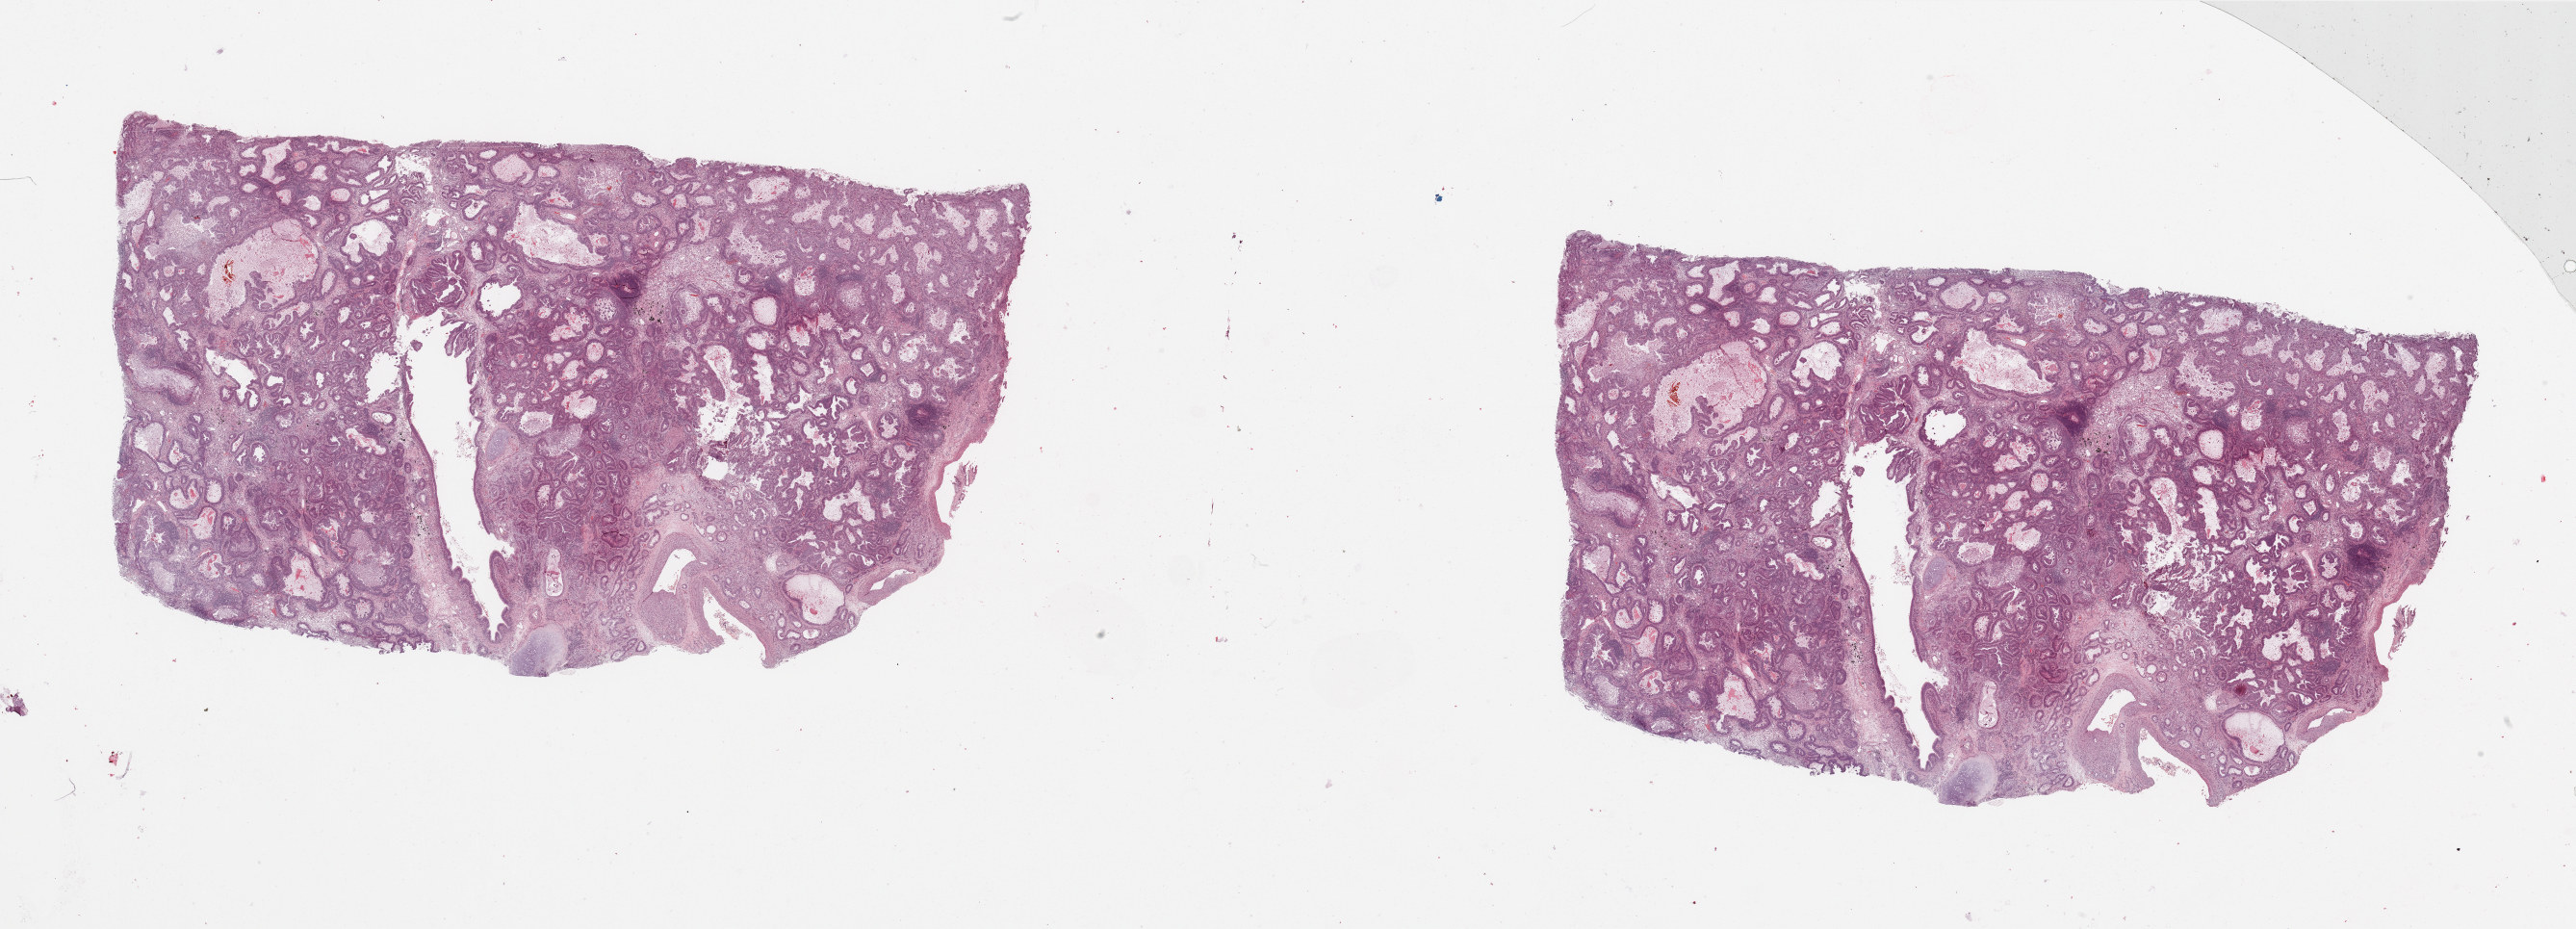
Digitized H&E tissue section (whole slide), low-resolution overview of the scanned area, about 42.3 x 15.3 mm. Lung, tissue type not recorded.
Patient diagnosis (cohort enrolment): lung adenocarcinoma (lung).